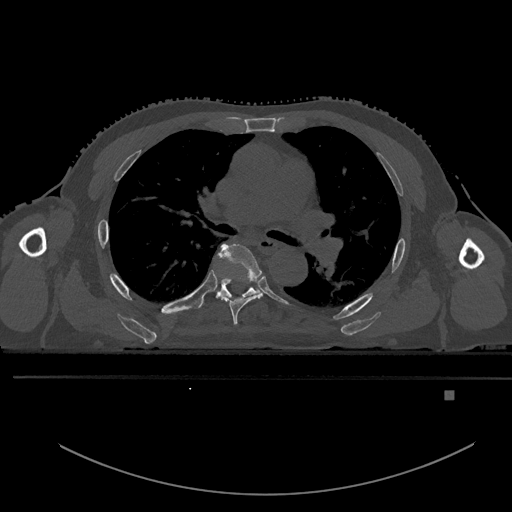
CT including the spine, one axial slice. Slice 337 of 969 in the series (ordered by position). Bone window (W 1800 / L 400 HU). 0.5 mm slice thickness. 512 × 512 image matrix. Male patient, age 82 years. From the clinical record (not read from this slice): primary cancer: prostate.
Structures marked on this image (semi-automatic segmentation, software-assisted and operator-edited):
- T5 vertebra: bounding box <214,243,262,326> (left, top, right, bottom; pixels)
- T6 vertebra: <198,278,259,309>